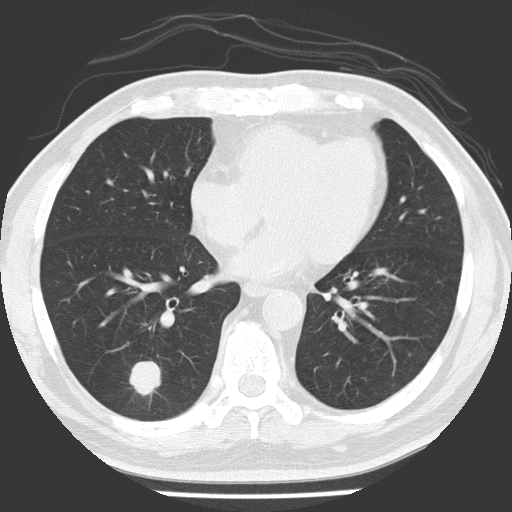
Low-dose screening chest CT, axial slice, baseline annual screen, lung window (W 1500 / L -600 HU), 2 mm slice thickness, slice 90 of 154 in the series. Male participant, aged 56 years at enrolment.
Expert reader's lesion annotation, bounding box [x1, y1, x2, y2] px = [114, 350, 167, 403]. Reader record for this screening exam (exam-level; its link to the box is not recorded): non-calcified nodule or mass ≥4 mm, right lower lobe, 21 × 17 mm, spiculated (stellate) margins, soft tissue attenuation. Participant outcome: lung cancer diagnosed 84 days after this screen — adenocarcinoma, NOS, right lower lobe, poorly differentiated (G3), stage IA (AJCC 6th edition), 24 mm at pathology.